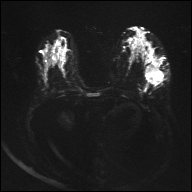
Breast MRI, one axial slice; slice 17 of 32 in the series (ordered by position); diffusion-weighted series; image 2 of 4 stored at this slice position (different b-values; order by instance number); 1.5 T; 4 mm slice thickness; 192 × 192 image matrix. Female patient.
Outlined on this slice (manually delineated by an expert):
- tumour on diffusion-weighted imaging: bounding box <147,66,162,80> (left, top, right, bottom; pixels)